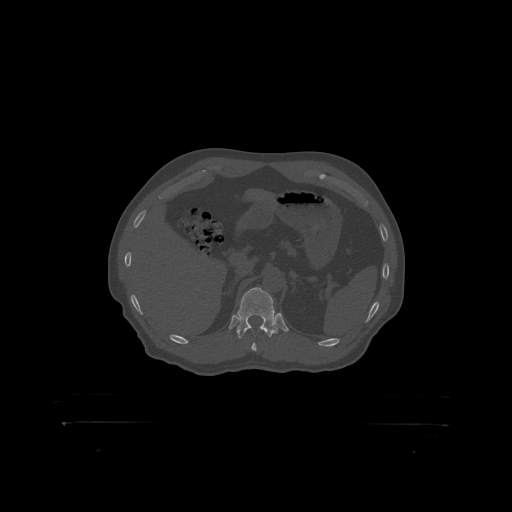
CT including the spine, one axial slice. Position 359 of 399 along the scan axis. Reconstruction kernel STANDARD. Bone window (W 1800 / L 400 HU). 1.25 mm slice thickness. 512 × 512 image matrix. Male patient, age 46 years. Case-level facts recorded for this patient, not image findings: primary cancer: skin.
Structures marked on this image (semi-automatically segmented with operator editing):
- T12 vertebra: bounding box (x1, y1, x2, y2) in pixels: (238, 288, 281, 319)